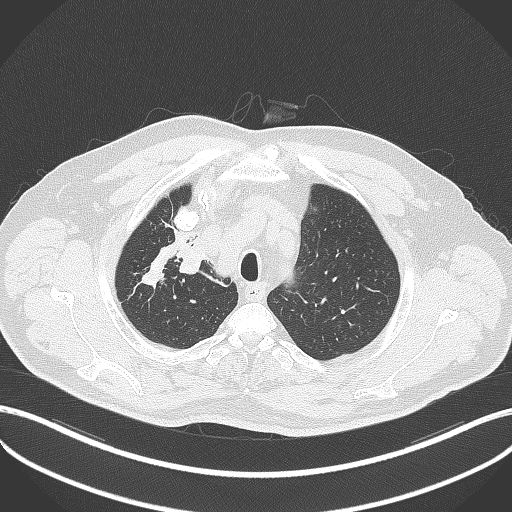
Chest CT, one axial slice. Position 320 of 411 along the scan axis. 120 kVp. Lung window (W 1500 / L -600 HU). 512 × 512 image matrix, field of view 400 × 400 mm. Patient: male, 60 years. From the clinical record (not read from this slice): clinical TNM (as recorded): T1b N1 M0.
Annotated regions visible in this slice (rectangle marked by the reading radiologist):
- lung tumour (recorded histology: squamous cell carcinoma): bounding box [x1, y1, x2, y2] px = [177, 231, 208, 278]